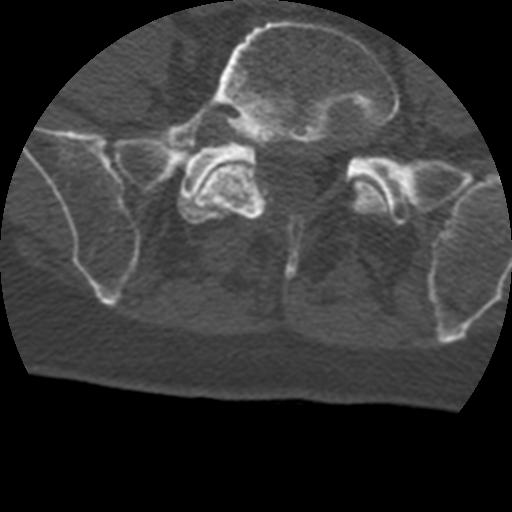
CT including the spine, one axial slice. Position 36 of 399 along the scan axis. Reconstruction kernel STANDARD. Bone window (W 1800 / L 400 HU). 512 × 512 image matrix, field of view 160 × 160 mm. Patient age 69 years. From the clinical record (not read from this slice): primary cancer: prostate.
Annotated regions visible in this slice (semi-automatic segmentation, software-assisted and operator-edited):
- L5 vertebra: bounding box (x1, y1, x2, y2) in pixels: (151, 20, 400, 280)